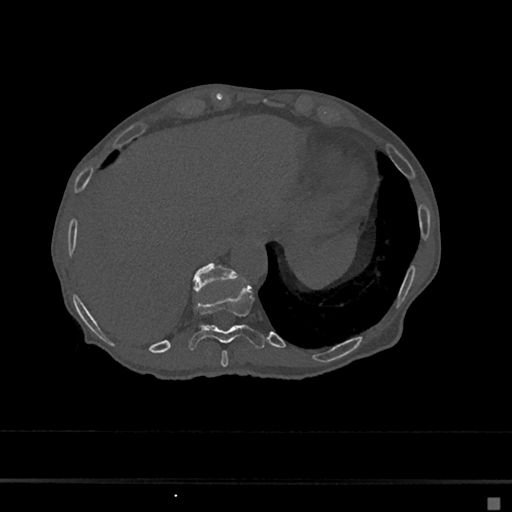
CT including the spine, one axial slice; slice 220 of 797 in the series (ordered by position); reconstruction kernel Br40s/3; bone window (W 1800 / L 400 HU); 512 × 512 image matrix, field of view 360 × 360 mm. Female patient, age 68 years. Case-level facts recorded for this patient, not image findings: primary cancer: renal.
Outlined on this slice (semi-automatic segmentation, software-assisted and operator-edited):
- T10 vertebra: bounding box [x1, y1, x2, y2] px = [188, 286, 265, 351]
- T11 vertebra: [192, 263, 237, 293]
- T9 vertebra: [220, 350, 229, 367]